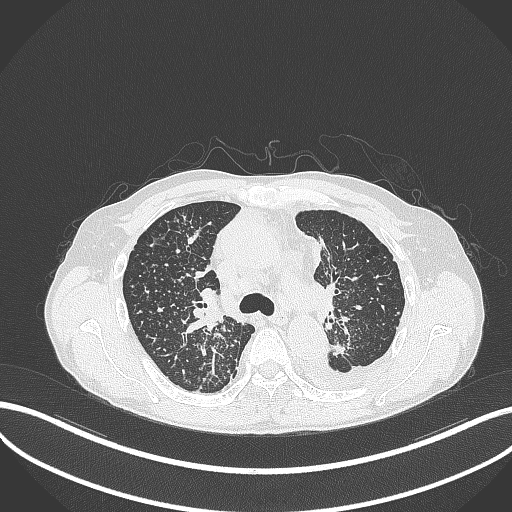
Chest CT, one axial slice; slice 243 of 325 in the series (ordered by position); reconstruction kernel B70f; 120 kVp; lung window (W 1500 / L -600 HU); 512 × 512 image matrix, field of view 400 × 400 mm. Patient: male, 58 years. Case-level facts recorded for this patient, not image findings: clinical TNM (as recorded): T1c N3 M1.
Outlined on this slice (bounding box drawn by a radiologist):
- lung tumour (recorded histology: adenocarcinoma): bounding box (x1, y1, x2, y2) in pixels: (329, 340, 348, 359)